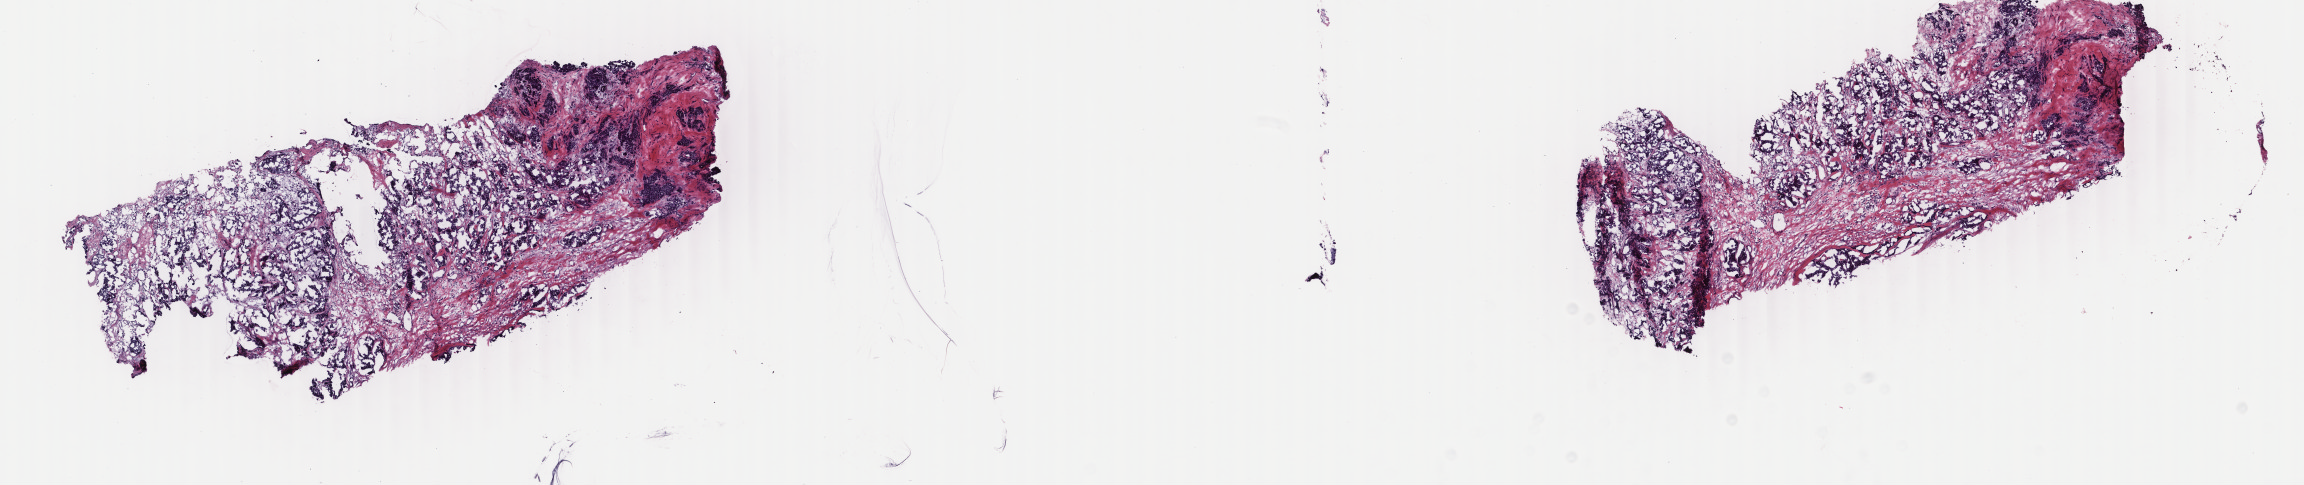
Digitized Hematoxylin and eosin (H&E) stained tissue section (whole slide) — shown as a low-resolution overview of the whole scanned area (about 18.3 x 3.9 mm); frozen section from the top of the tissue portion; primary tumour sample from the breast. Female, age 67 years at initial diagnosis. Composition of this section per pathologist review: tumour cells 80%, tumour nuclei 80%, normal cells 0%, stromal cells 20%, necrosis 0%. Inflammatory infiltration, as recorded: lymphocyte infiltration 2%, monocyte infiltration 1%, neutrophil infiltration 1%.
* pathologic diagnosis: Infiltrating duct carcinoma, NOS
* lymph nodes positive (case pathology): 4 of 7 examined
* AJCC pathologic stage: IIB (4th edition)